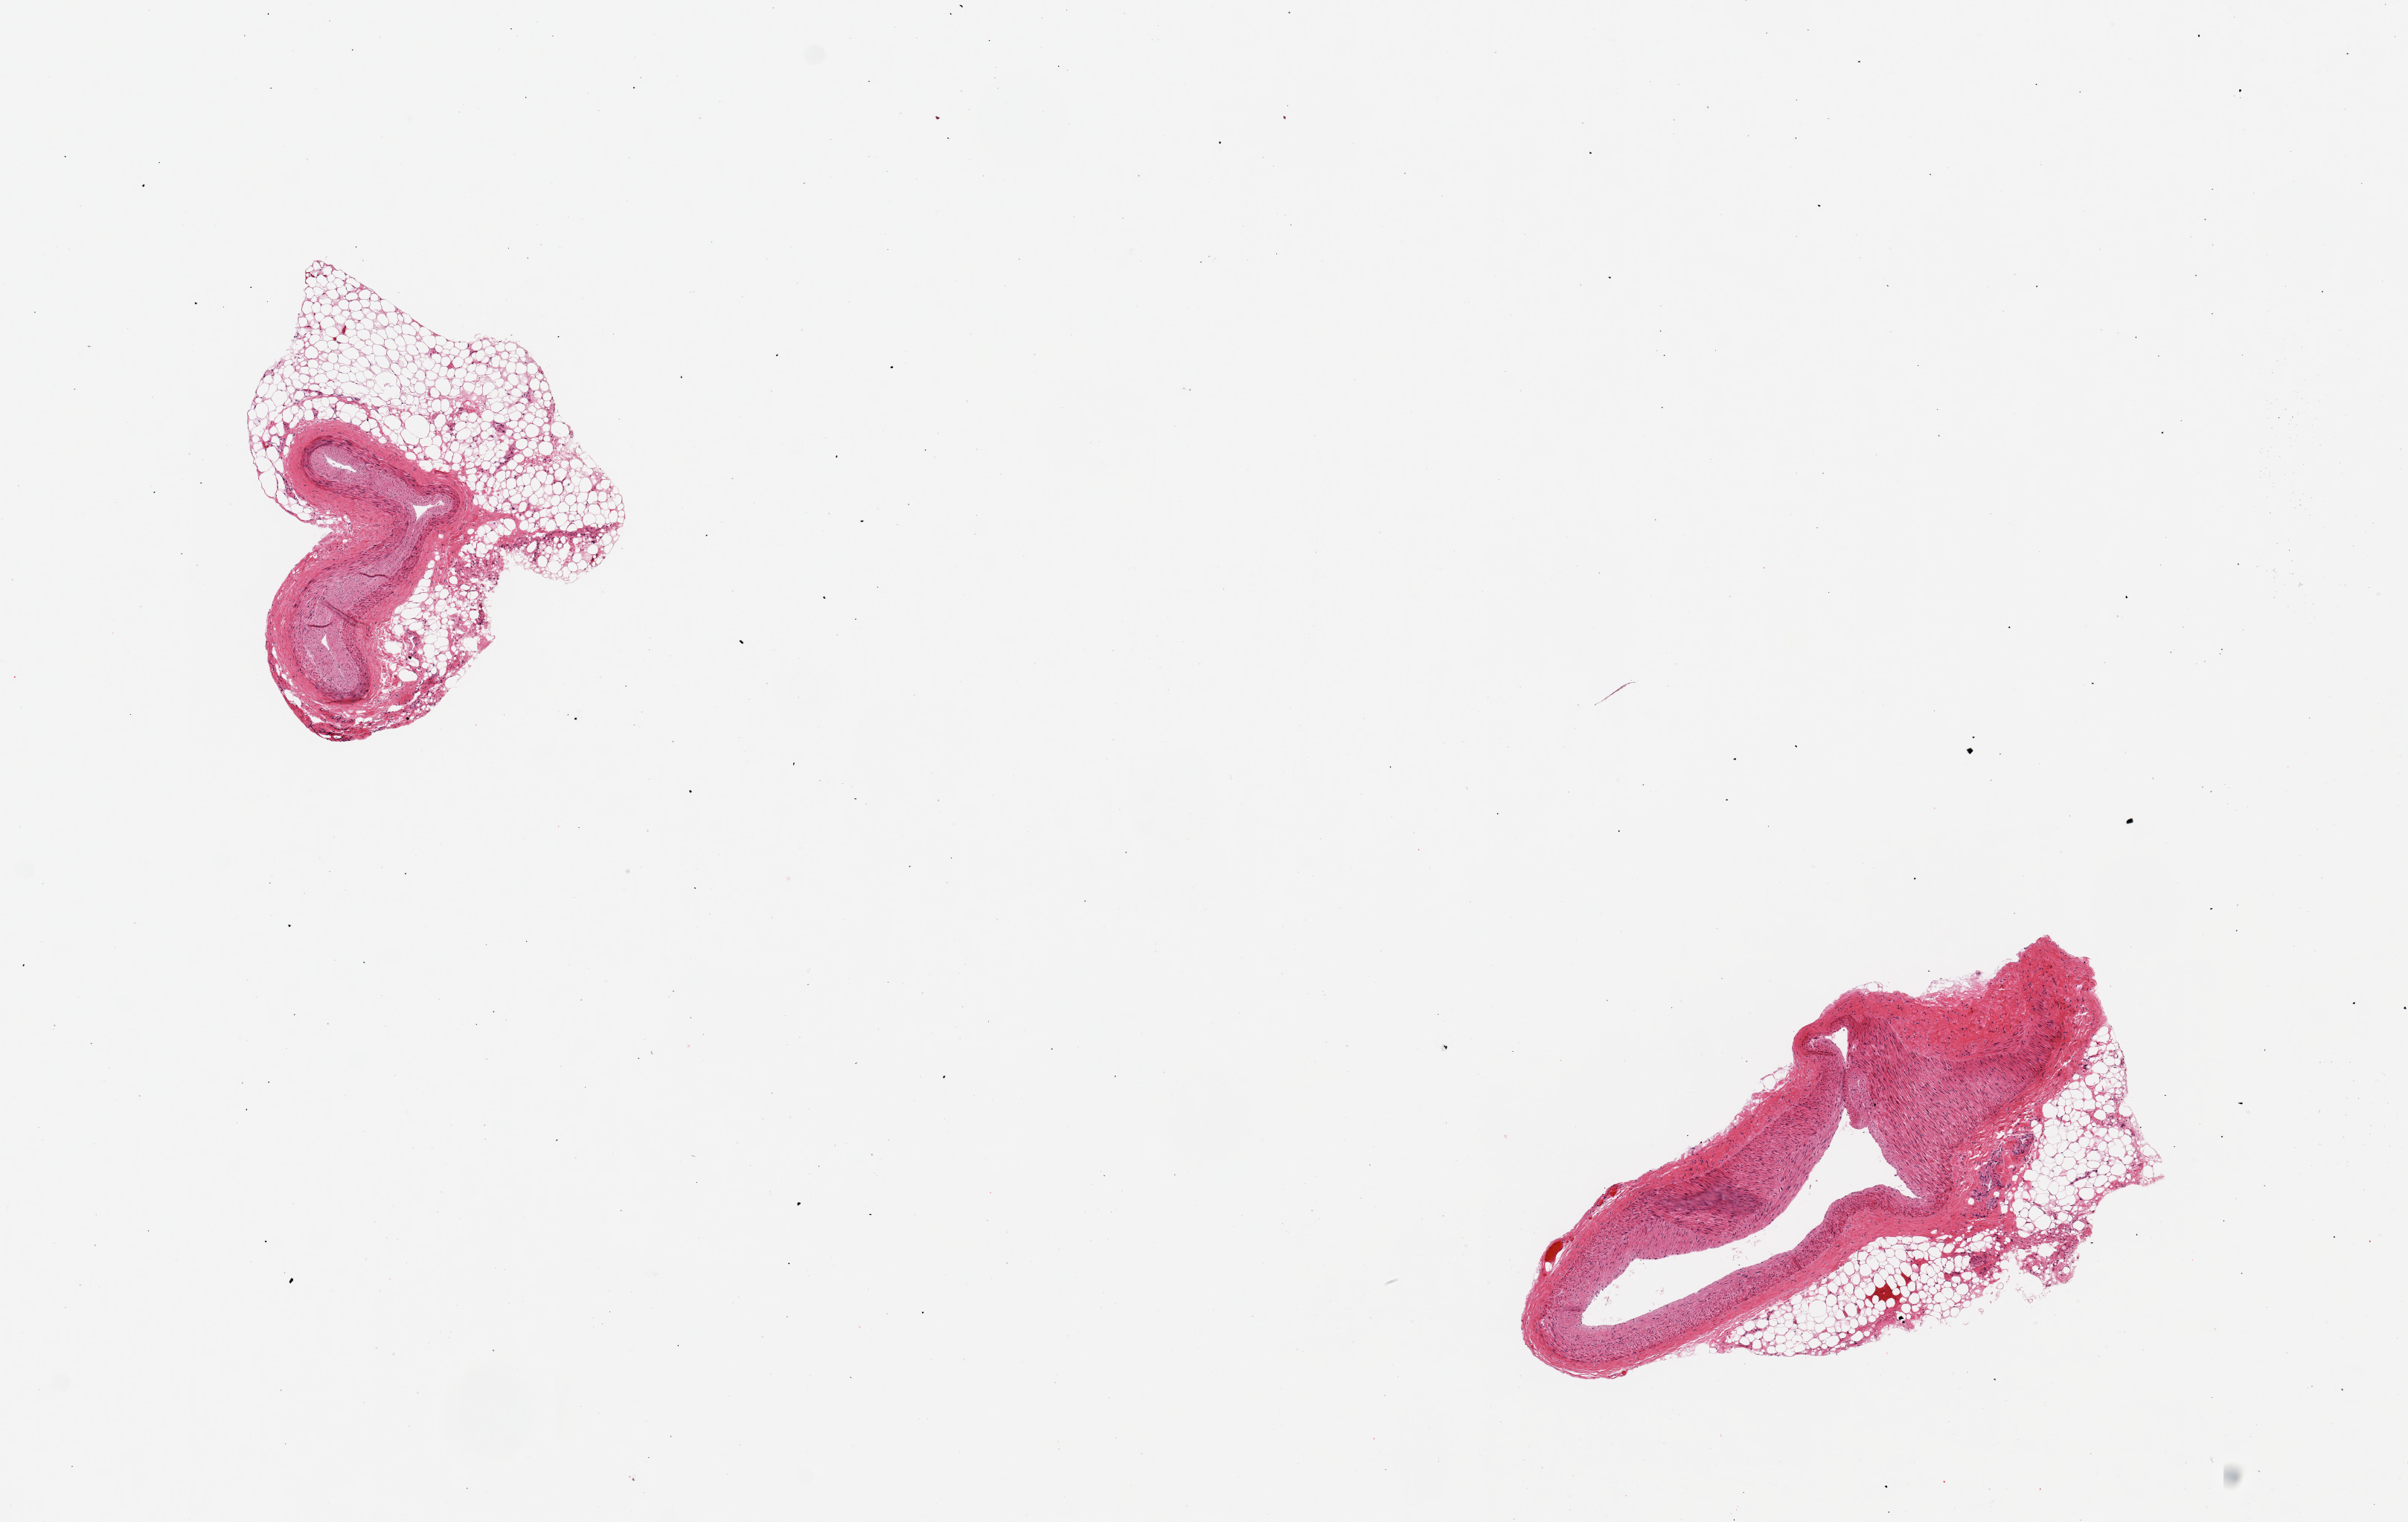
Digitized hematoxylin and eosin (H&E)-stained section, a low-resolution overview of the entire scanned area, about 12.8 x 8.1 mm. PAXgene-fixed paraffin-embedded (PFPE) section. Sampled site (target tissue): coronary artery. Tissue donor sample. Donor: female.
Pathologist's review note for this sample: 2 pieces ~1.5mm d; Discontinuous adherent fat up to ~0.5mm.